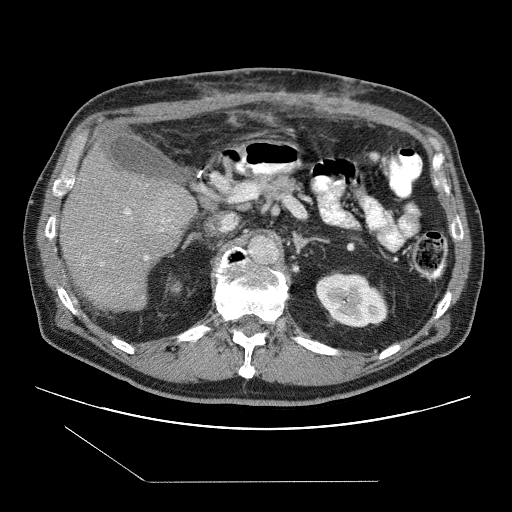
Contrast-enhanced abdominal CT (liver protocol), one axial slice; slice 49 of 109 in the series (ordered by position); reconstruction kernel STANDARD; one of 2 acquisitions stored at this slice position; soft-tissue window (W 400 / L 40 HU); 512 × 512 image matrix. From the clinical record (not read from this slice): diagnosis: hepatocellular carcinoma (patient treated with transarterial chemoembolisation; whether this scan precedes or follows treatment is not stated here); TNM stage (as recorded): Stage-IIIB; Child-Pugh class: A; tumour differentiation: well differentiated.
Structures marked on this image (semi-automatic segmentation, software-assisted and operator-edited):
- liver parenchyma outside the tumour (the mass and vessels are separate outlines, so this box may not span the whole liver): bounding box (x1, y1, x2, y2) in pixels: (58, 144, 196, 310)
- liver vessels: (100, 209, 171, 265)